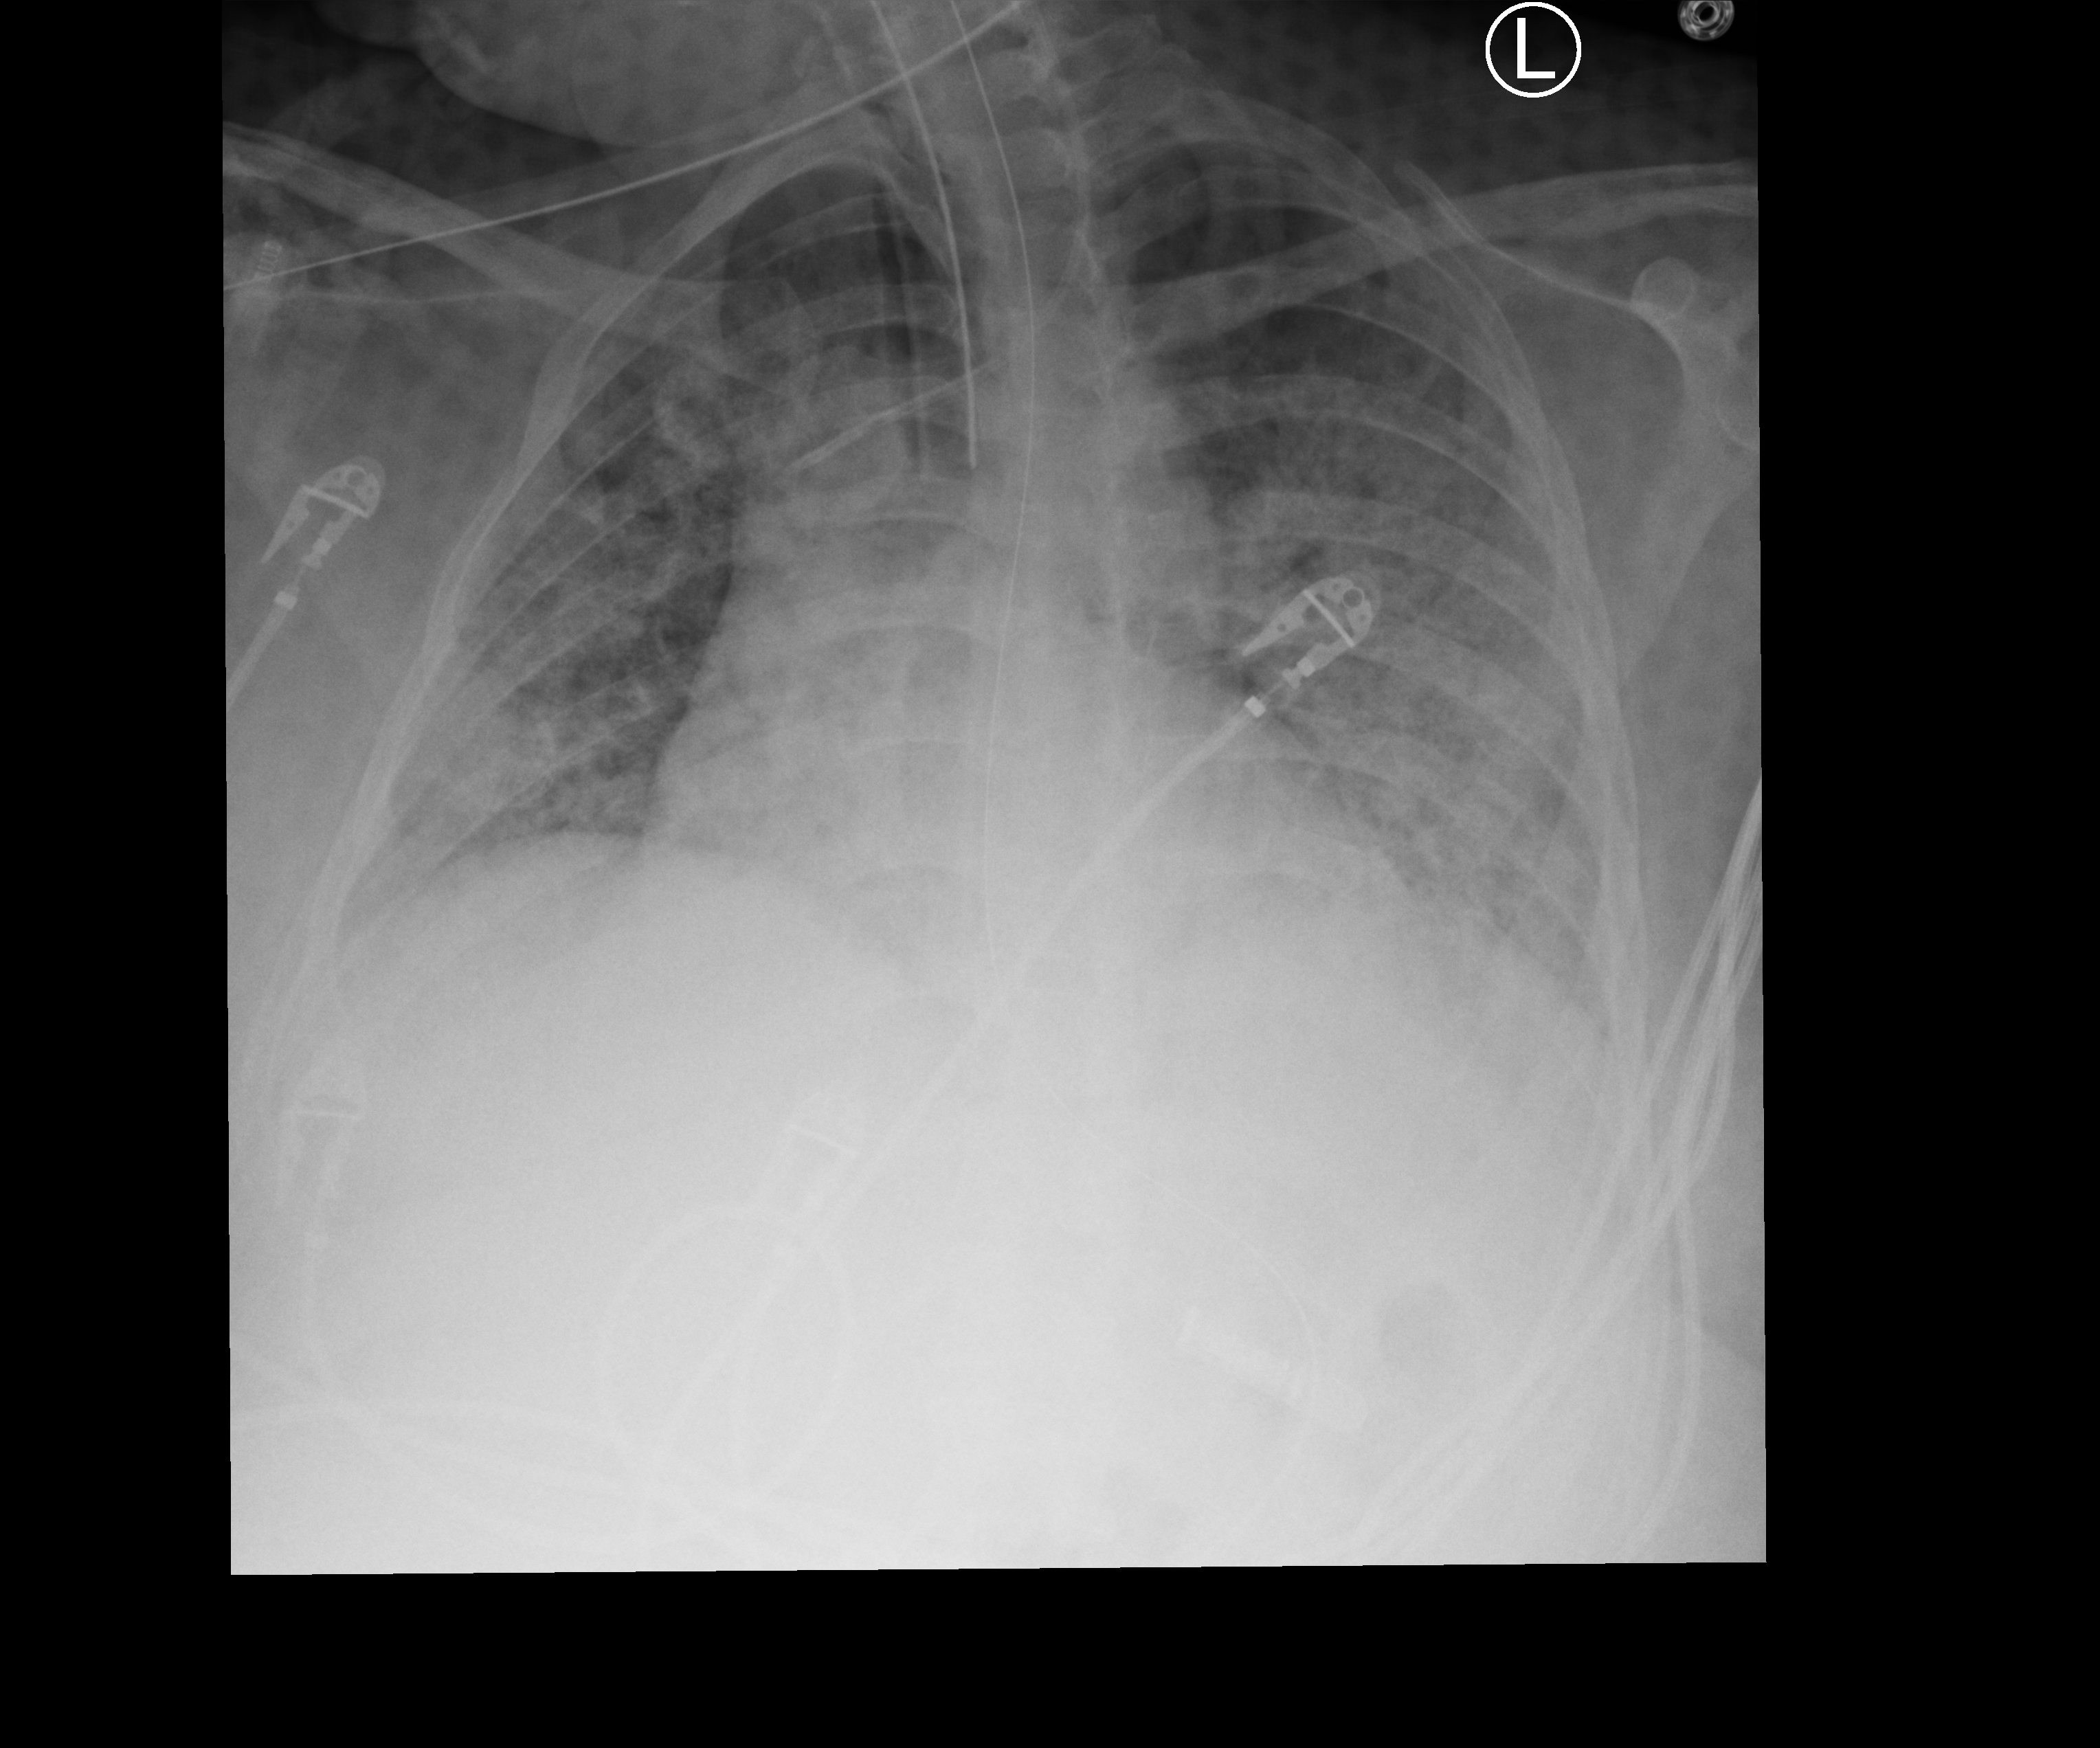
Chest X-ray (portable), anteroposterior (AP) projection. Female patient hospitalised with COVID-19, age 18–59 years.
Hospital-stay facts (about this admission, not read from this image; timing relative to this image not recorded): length of hospital stay: 33 days; admitted to intensive care during this hospital stay: no.